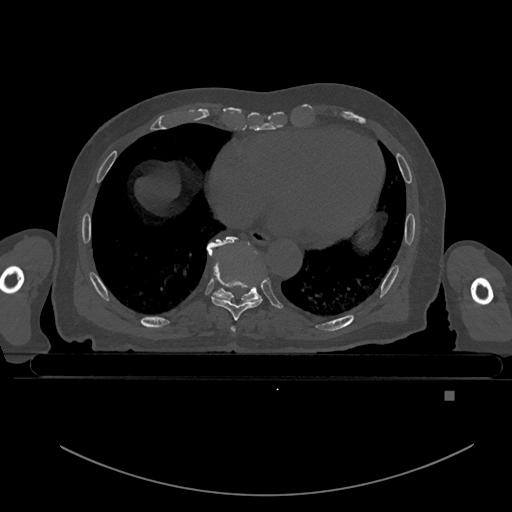
CT including the spine, one axial slice; bone window (W 1800 / L 400 HU); 0.5 mm slice thickness; 512 × 512 image matrix. Patient: male, 82 years. Case-level facts recorded for this patient, not image findings: primary cancer: prostate; vertebrae with lytic lesions (as recorded): T11, T9, T8, T2.
Structures marked on this image (semi-automatically segmented with operator editing):
- T7 vertebra: bounding box <231,326,236,333> (left, top, right, bottom; pixels)
- T8 vertebra: <212,256,263,321>
- T9 vertebra: <207,236,261,302>